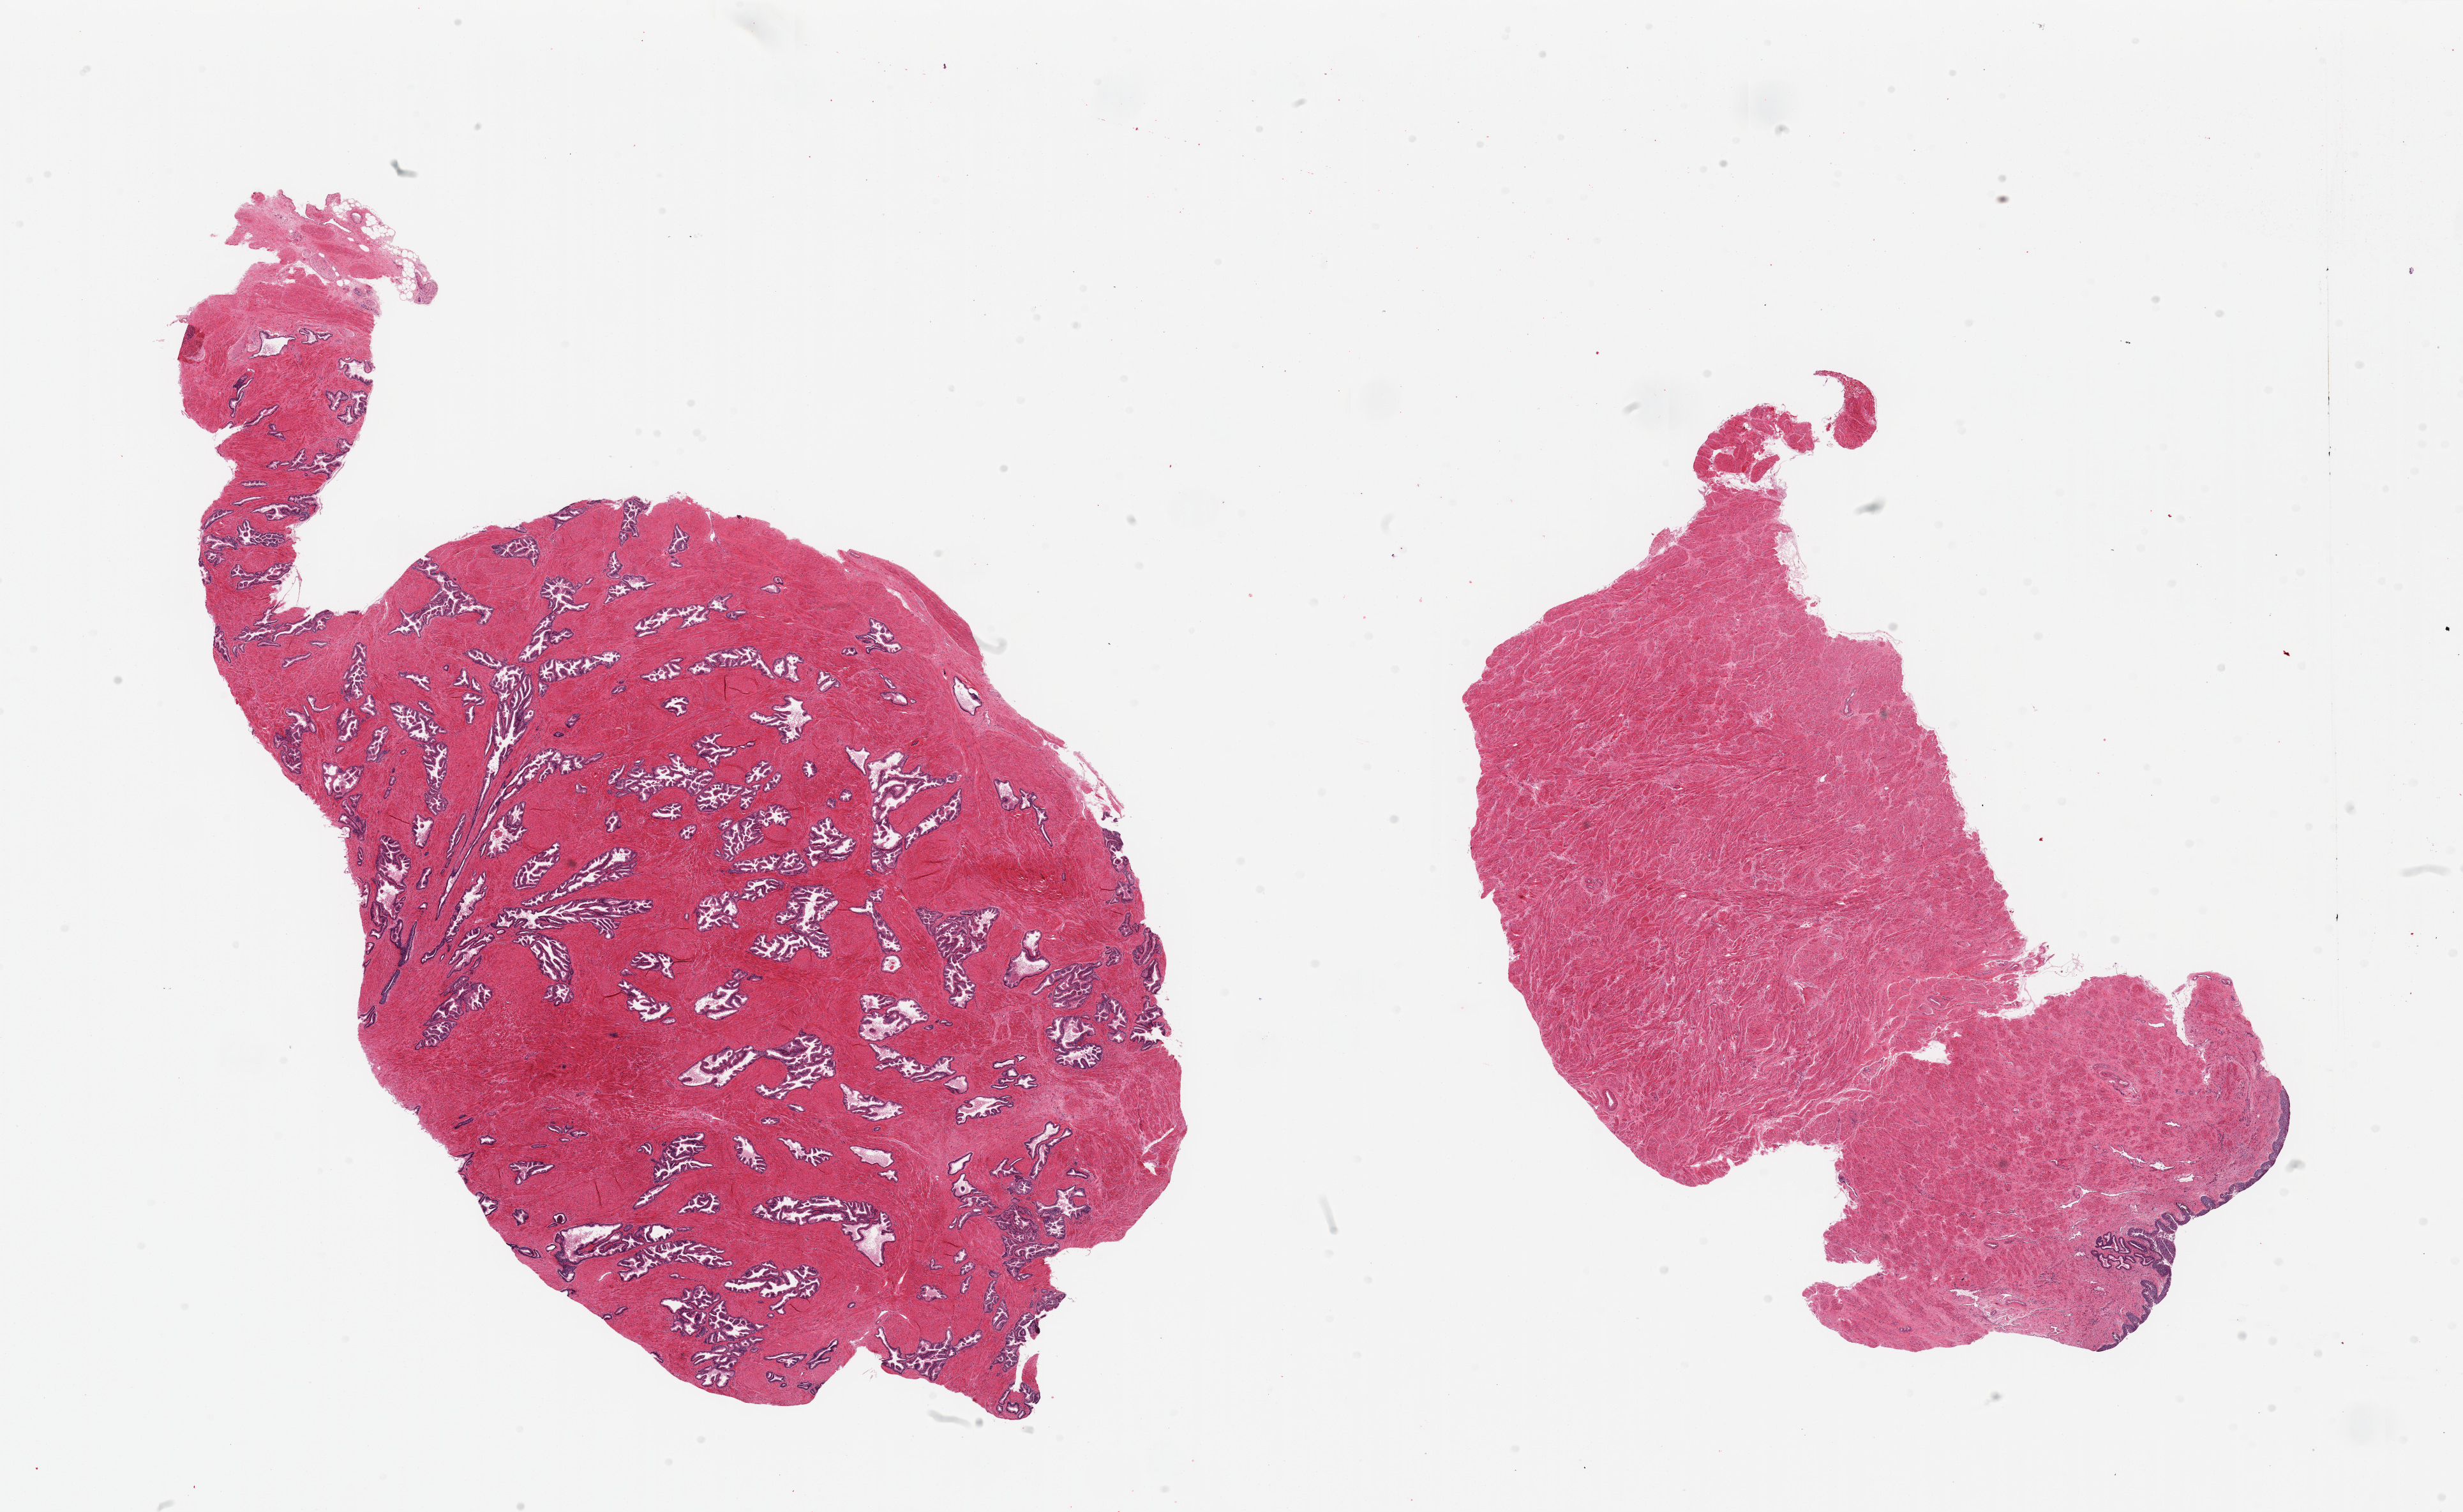
Haematoxylin and eosin whole-slide image, brightfield — whole scanned area (about 30.5 x 18.7 mm, slide scanned at 20x) shown as a low-resolution overview; PAXgene-fixed paraffin-embedded (PFPE) section; target tissue: prostate; tissue donor sample. Donor: male.
Reviewer comment on this tissue sample: 2 pieces, mild hyperplastic glandular pattern.